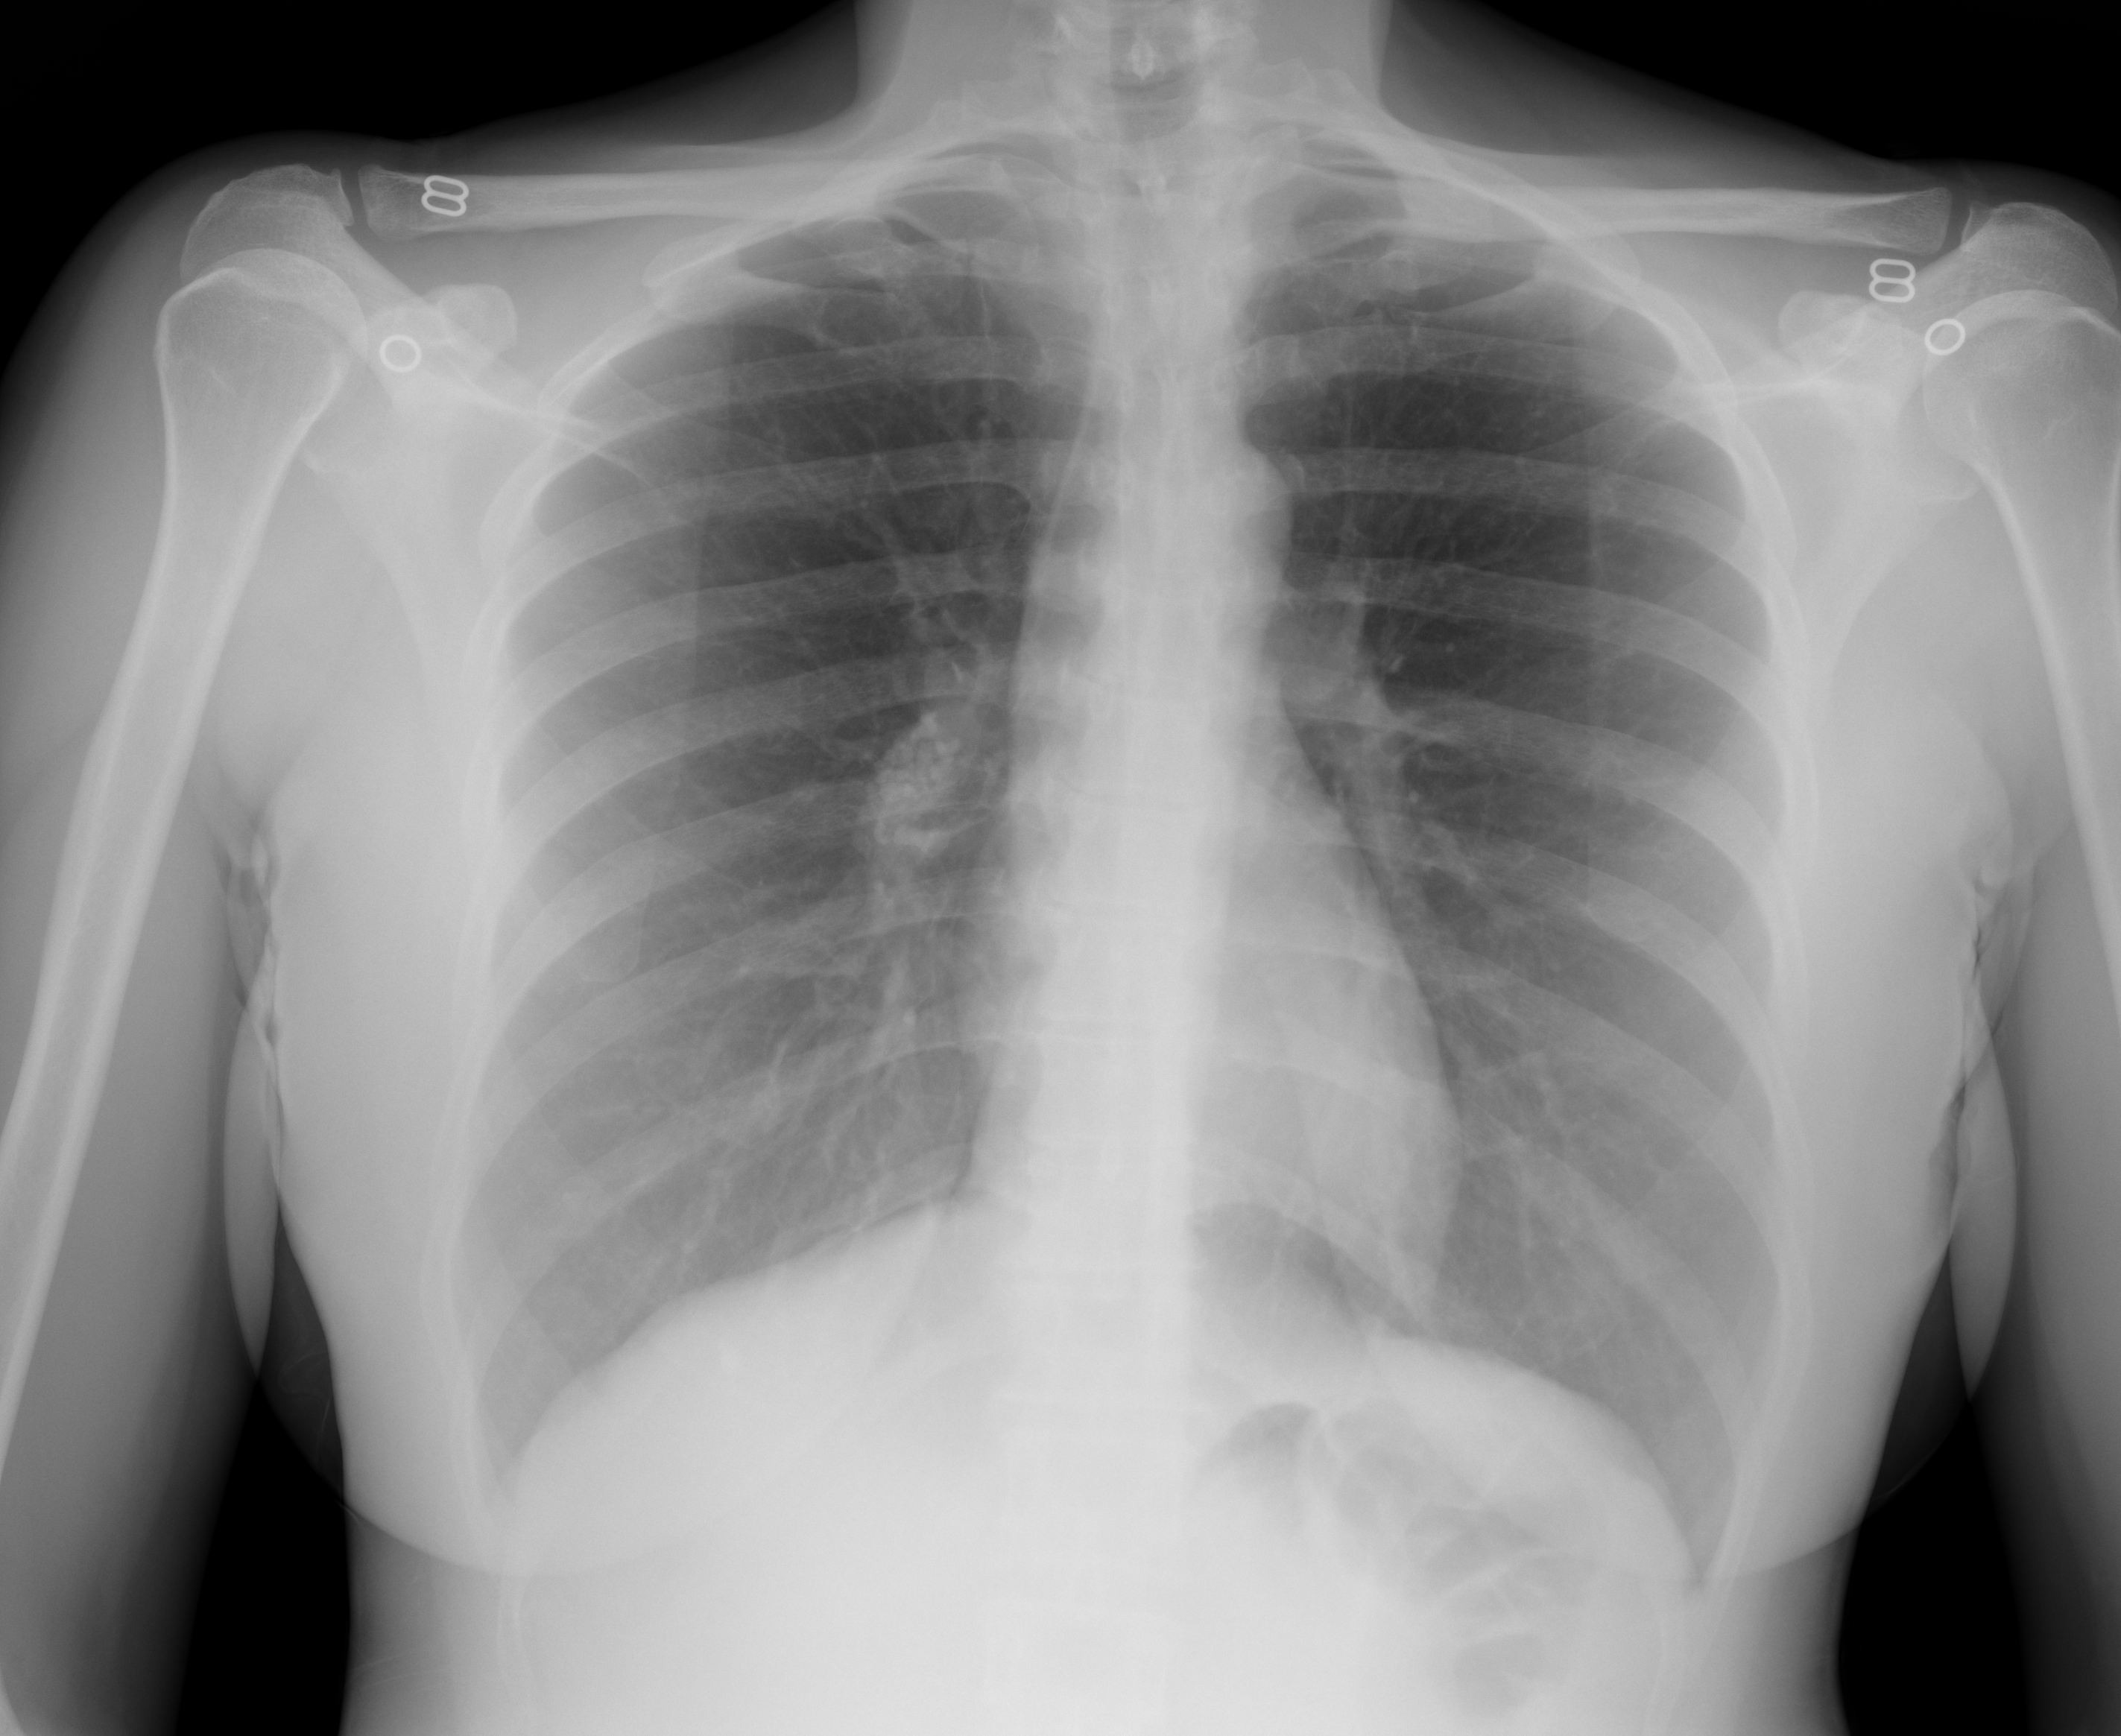
Chest X-ray (portable), AP projection. Female patient, age 48 years; imaged 1 day before the COVID-19 diagnosis.
Radiologist's key findings for this exam: Lungs are well inflated and clear, no nodule, airspace disease or pleural effusion.